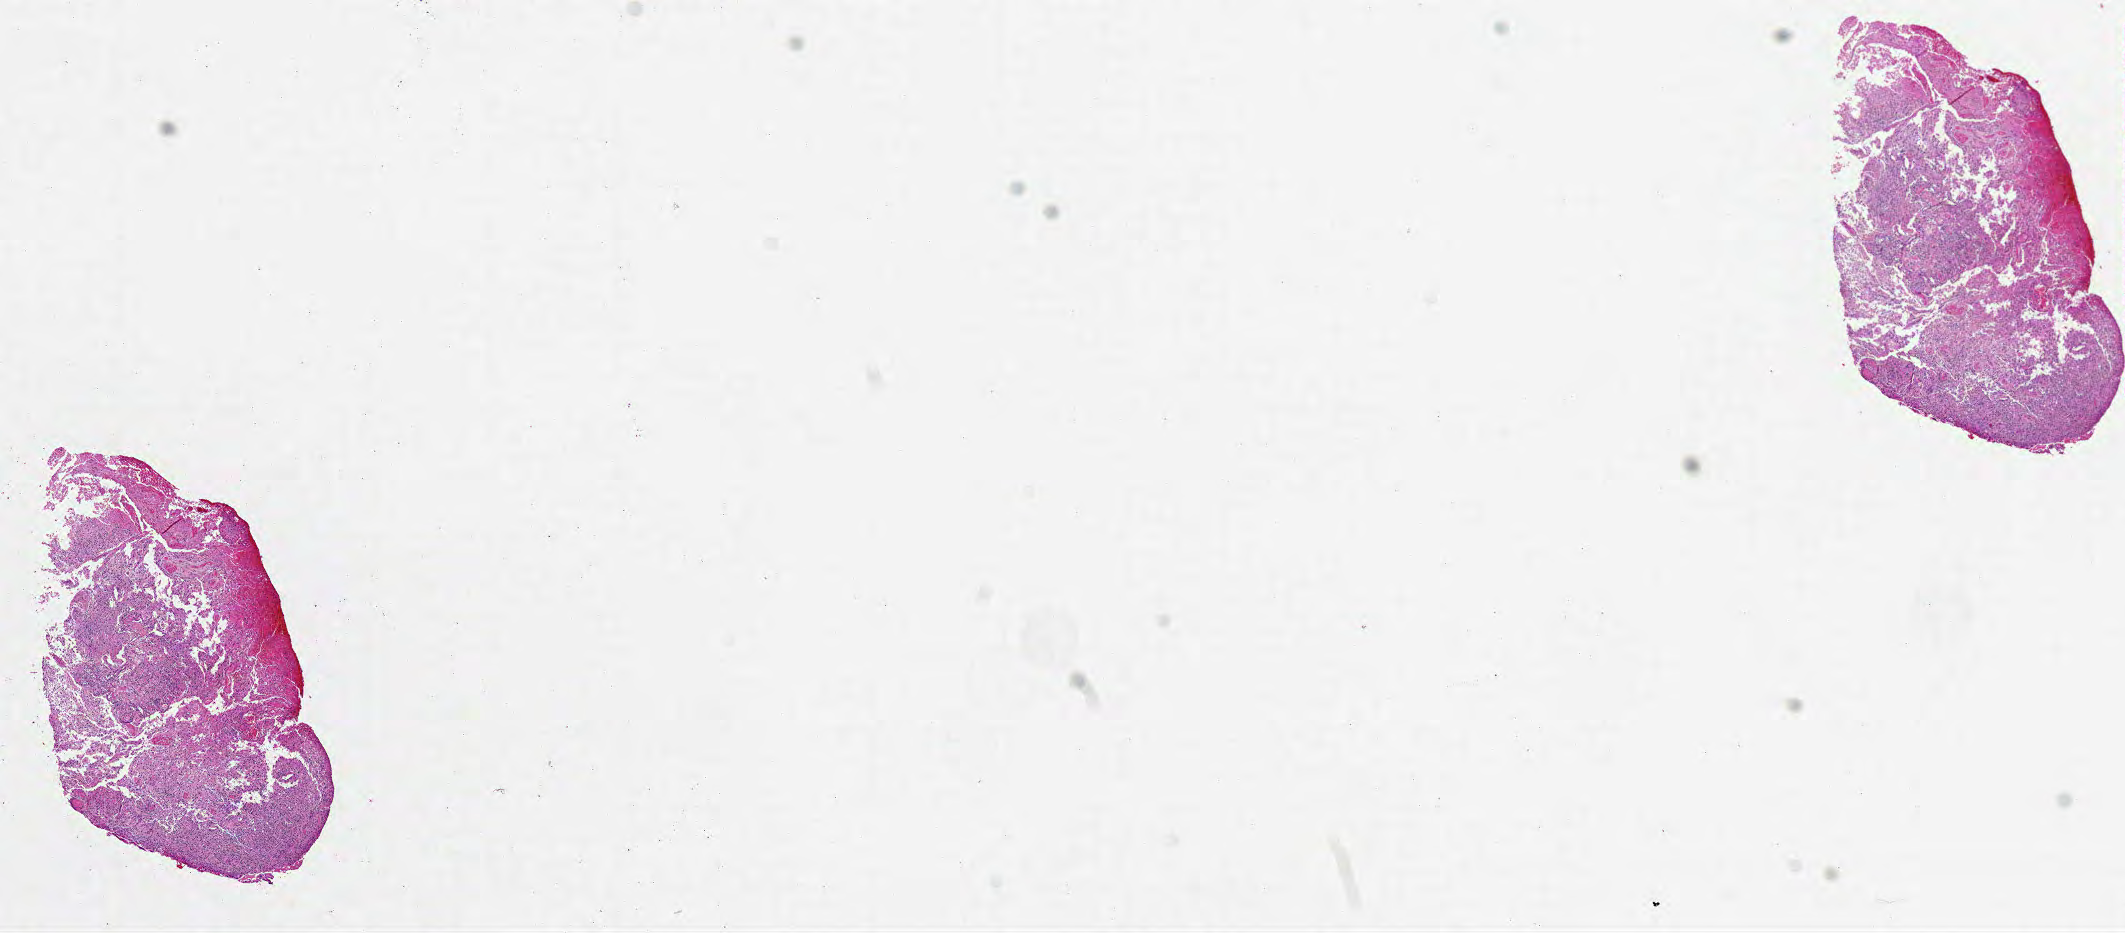
H&E whole-slide image — a low-resolution overview of the entire scanned area, about 17.0 x 7.5 mm (acquisition: 20x scan); FFPE section; brain, primary tumour sample. Male, age 57 years at initial diagnosis.
Diagnosis: Glioblastoma.